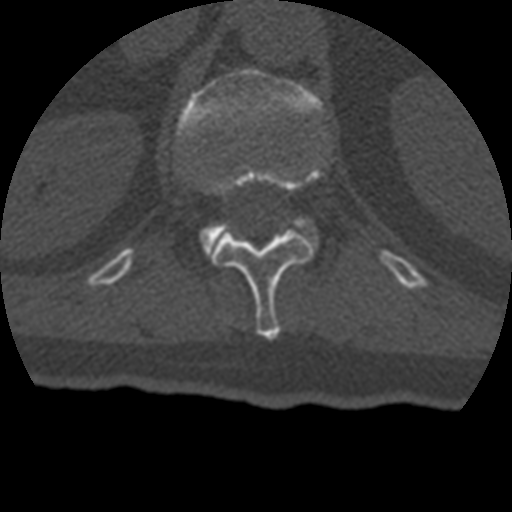
CT including the spine, one axial slice. Slice 162 of 399 in the series (ordered by position). Reconstruction kernel STANDARD. Bone window (W 1800 / L 400 HU). 1.25 mm slice thickness. 512 × 512 image matrix, field of view 160 × 160 mm. Patient age 69 years. From the clinical record (not read from this slice): primary cancer: prostate.
Structures marked on this image (semi-automatic segmentation, software-assisted and operator-edited):
- L1 vertebra: box from (x=177, y=68) to (x=324, y=257) px
- T12 vertebra: (x=213, y=173)–(x=314, y=340)